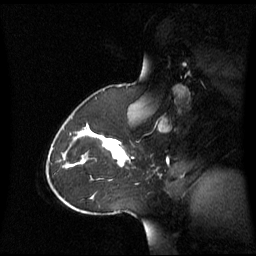
Breast MRI (dynamic contrast-enhanced), one sagittal slice. Slice 43 of 60 in the series (ordered by position). Dynamic contrast-enhanced series, image 2 of 3 at this slice position (ordered by acquisition). 1.5 T. TE 4.2 ms, TR 8.4 ms. 2.8 mm slice thickness. 256 × 256 image matrix, field of view 270 × 270 mm. Patient: female, 43 years. Case-level facts recorded for this patient, not image findings: setting: breast cancer imaged before/during neoadjuvant chemotherapy; receptor status: triple-negative.
Structures marked on this image (semi-automatic segmentation, software-assisted and operator-edited):
- analysis volume of interest (the breast-tissue region the enhancement analysis was run in; not a lesion): bounding box (x1, y1, x2, y2) in pixels: (62, 124, 129, 180)
- tumour enhancement mask (voxels above the 70 % enhancement threshold inside the analysis volume of interest): (82, 124, 128, 166)